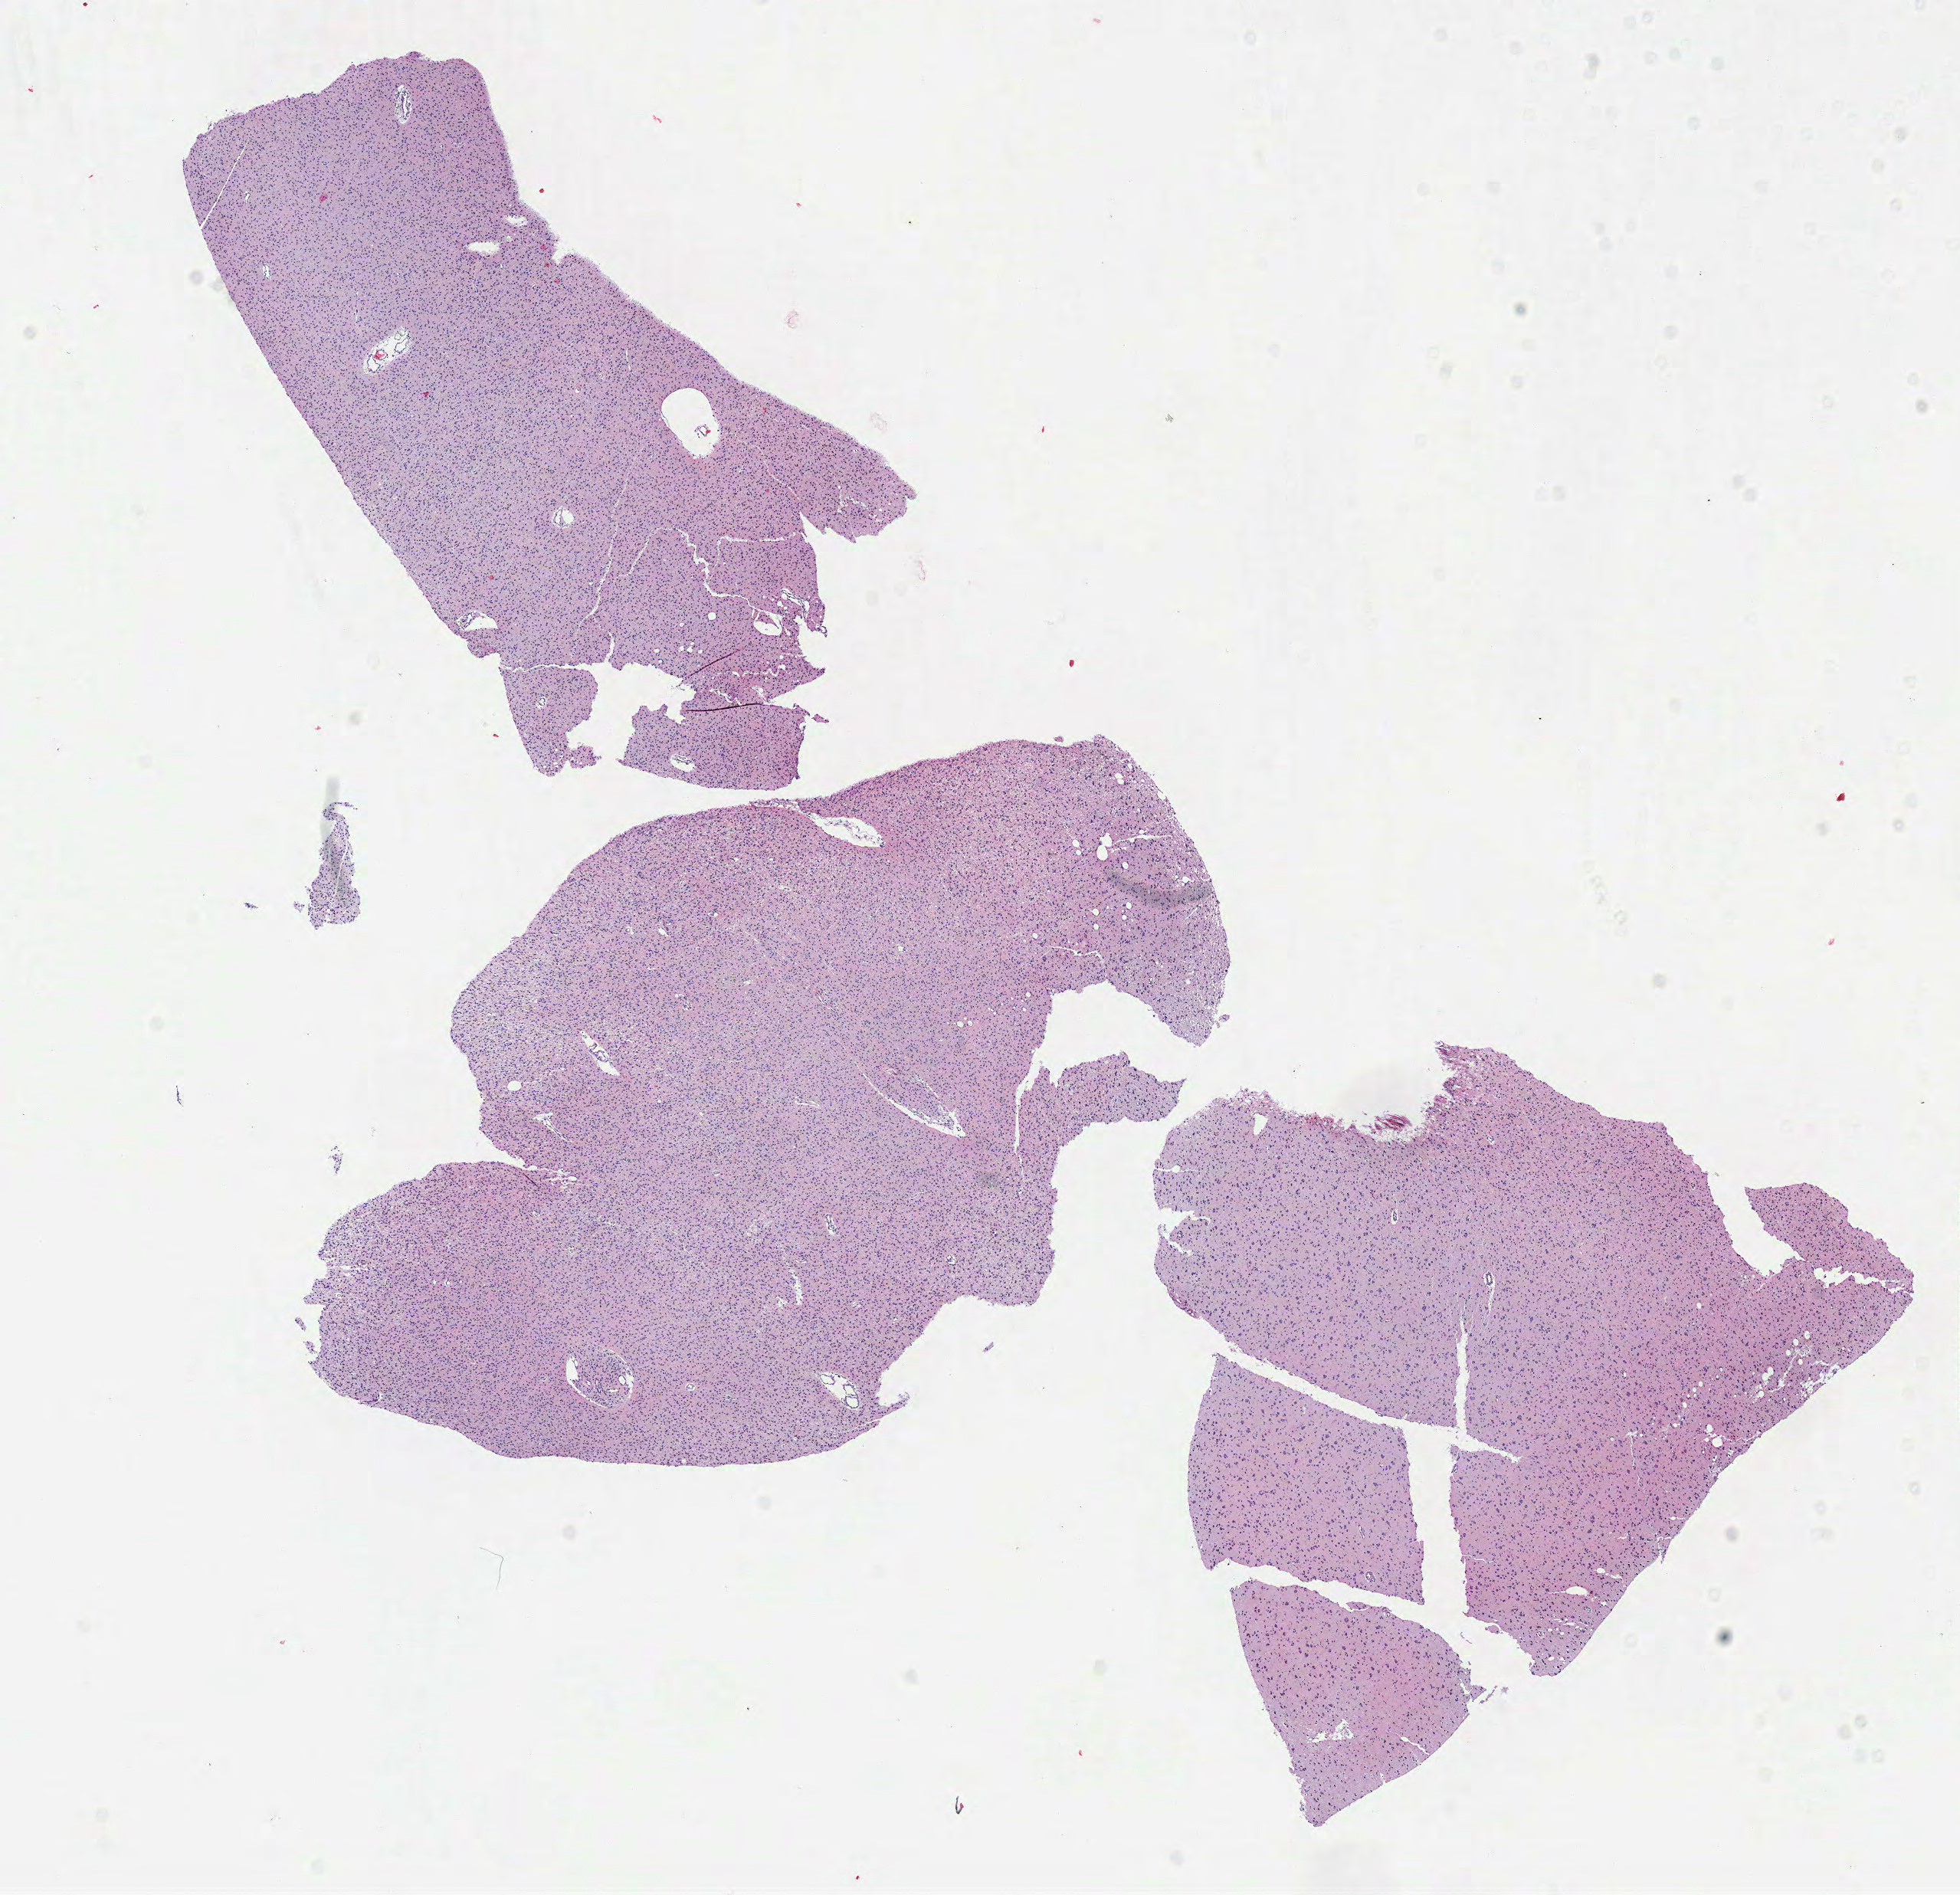
Digitized H&E tissue section (whole slide), shown as a low-resolution overview of the whole scanned area (about 10.1 x 9.7 mm, from a 40x scan); frozen section from the top of the tissue portion; sample: primary tumour, brain. Female patient; age at initial diagnosis 34 years. Slide review estimates, as recorded: tumour cells 100%, tumour nuclei 75%.
Histologic diagnosis: Oligodendroglioma, NOS.